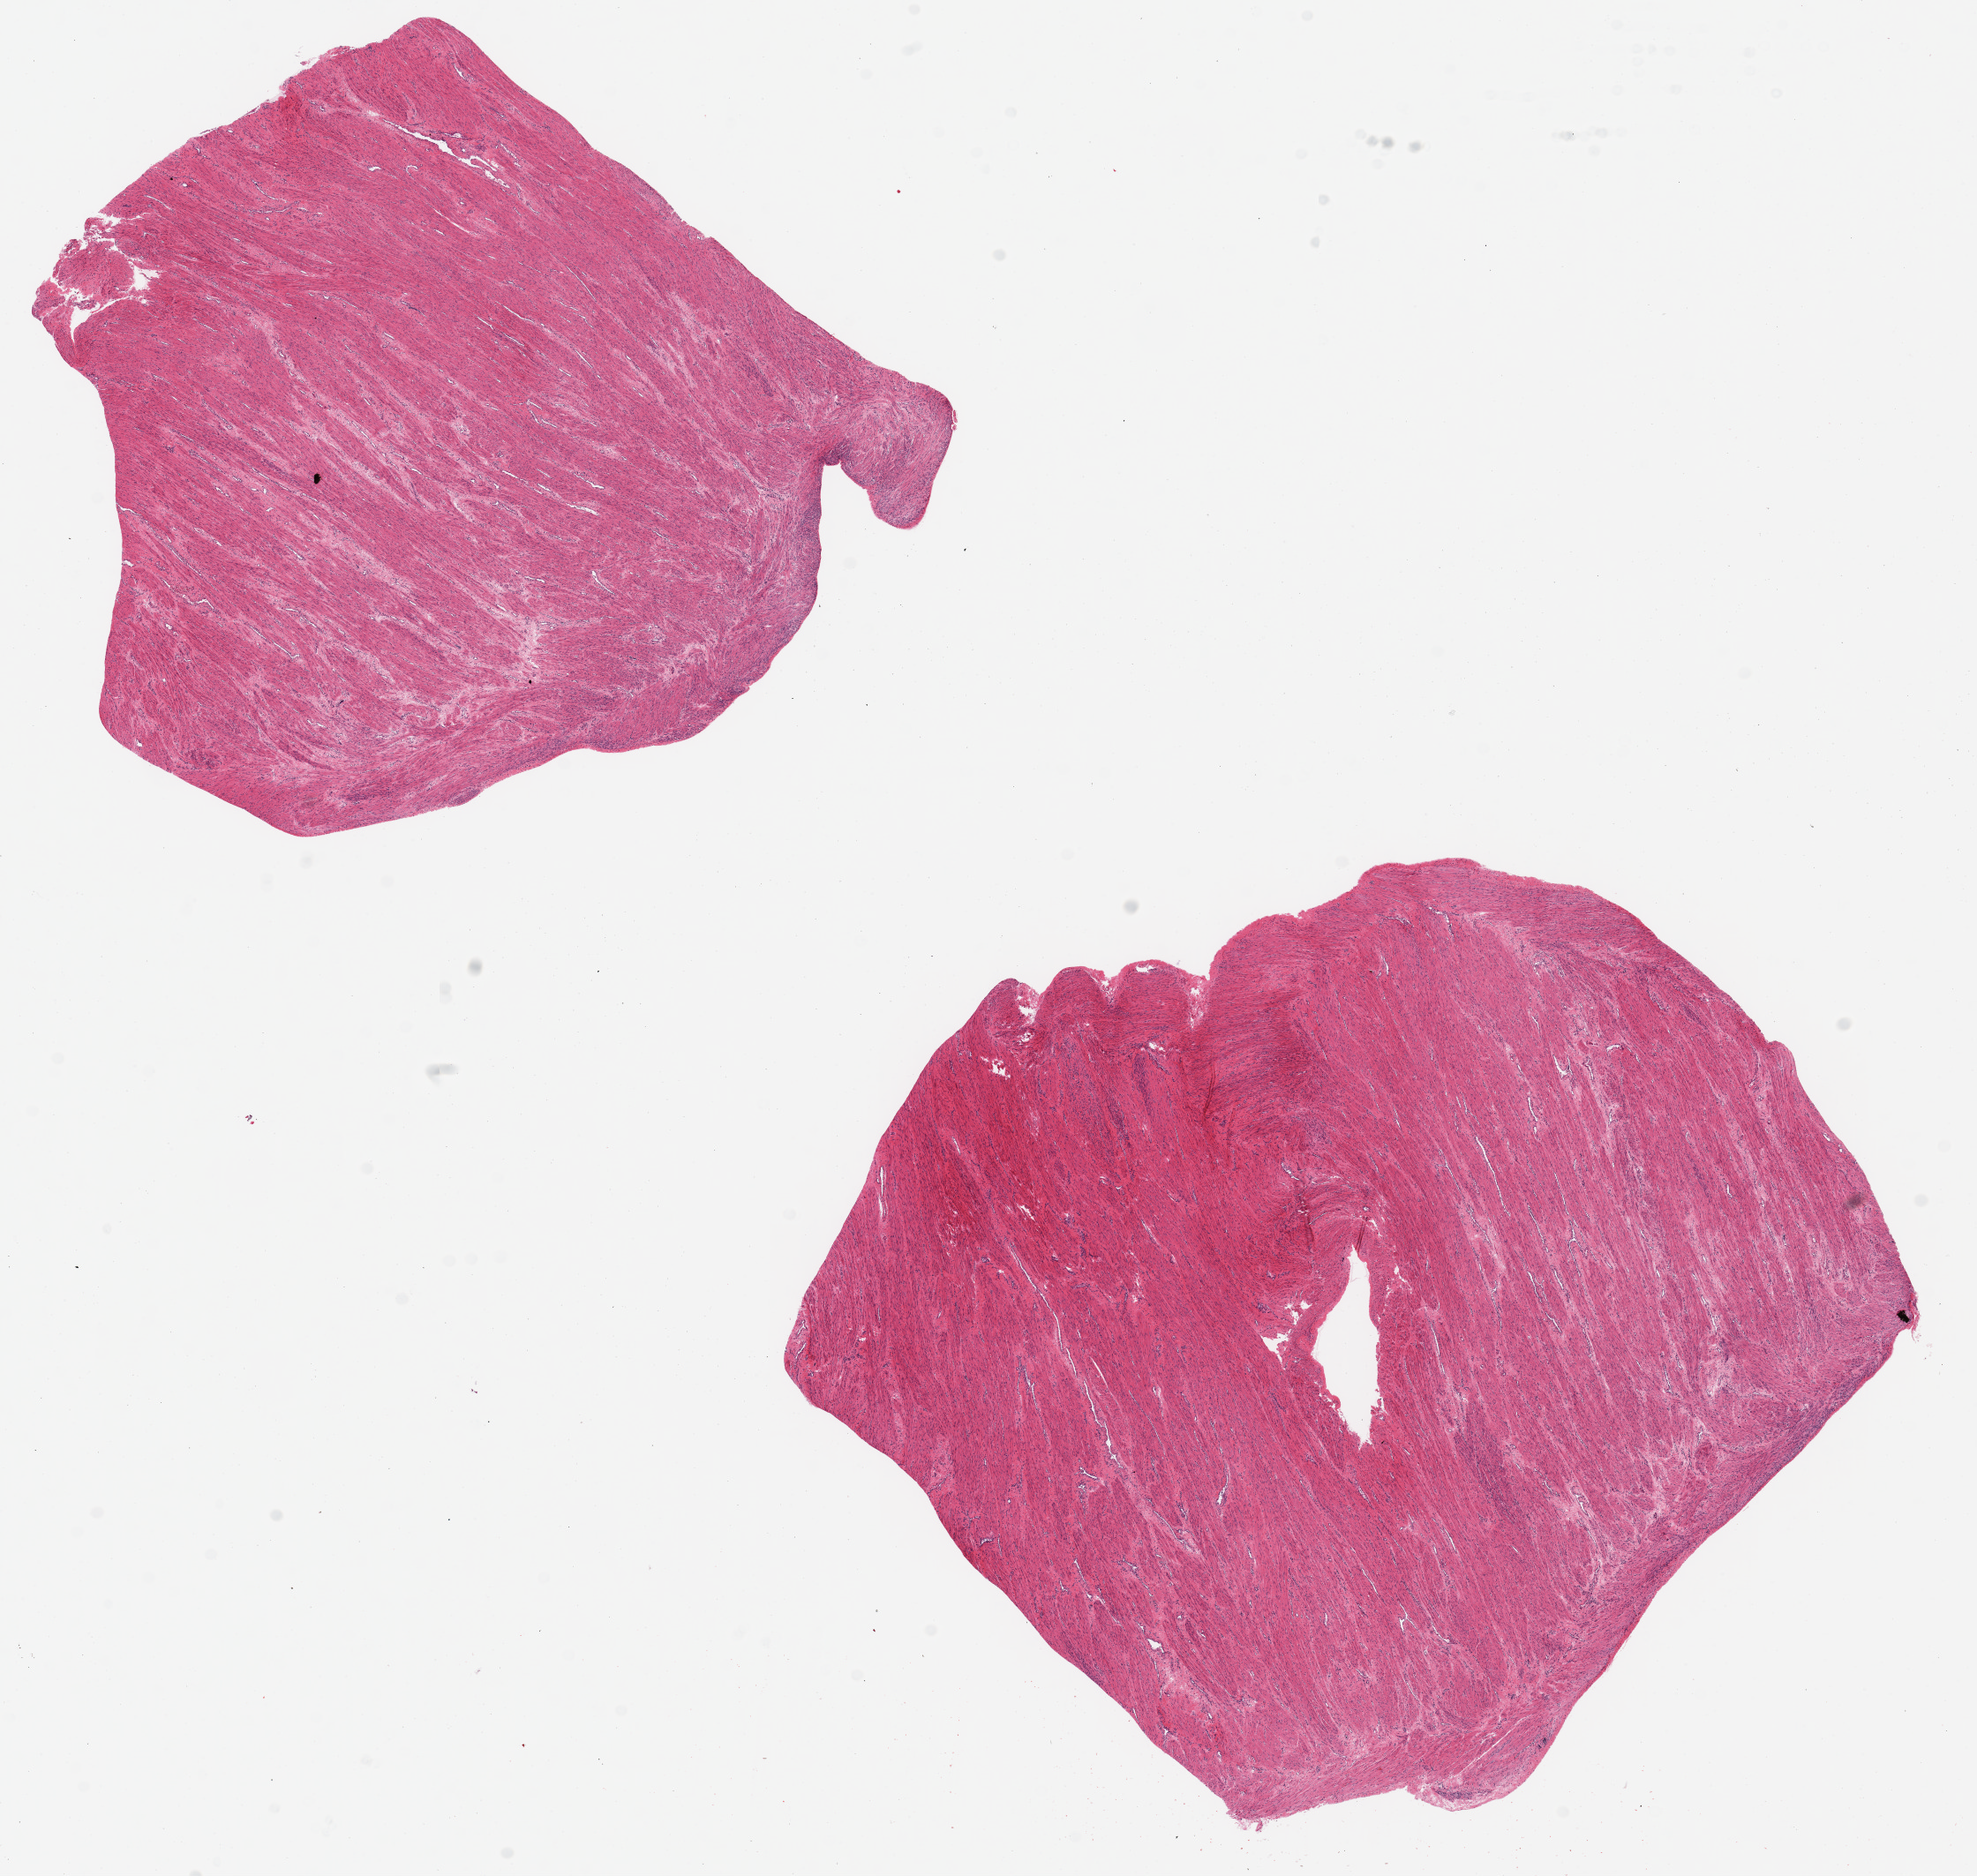
Digitized haematoxylin and eosin-stained section — shown as a low-resolution overview of the whole scanned area (about 17.7 x 16.8 mm, from a 20x scan), PAXgene-fixed paraffin-embedded (PFPE) section, sampled site (target tissue): uterus, donor tissue sample.
Review note (as recorded): 2 pieces, 7x7 & 10x8mm; no endoemtrium, all muscle.